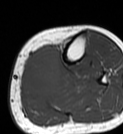
MRI of an extremity soft-tissue mass, one axial slice. Slice 22 of 68 in the series (ordered by position). MR volume resampled by the dataset authors to the PET/CT grid (not the native acquisition matrix). 123 × 134 image matrix, field of view 120 × 131 mm. Female patient. From the clinical record (not read from this slice): histological type: extraskeletal high grade osteogenic sarcoma; grade: high; site of the primary tumour: left calf.
Annotated regions visible in this slice (expert contour drawn on MRI and transferred to this co-registered scan by the dataset authors):
- gross tumour volume (mass): bounding box [x1, y1, x2, y2] px = [22, 46, 62, 101]